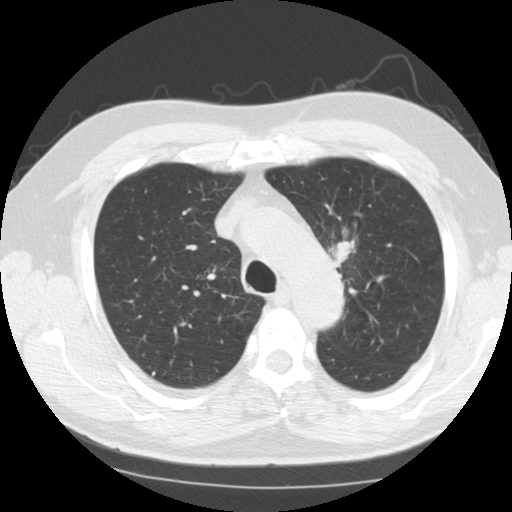
Low-dose screening chest CT, one axial slice; position 95 of 124 along the scan axis; lung window (W 1500 / L -600 HU); 512 × 512 image matrix, field of view 340 × 340 mm.
Structures marked on this image (manually delineated by an expert):
- lesion 1 (tumor, upper lobe of left lung): bounding box [x1, y1, x2, y2] px = [330, 241, 351, 266]